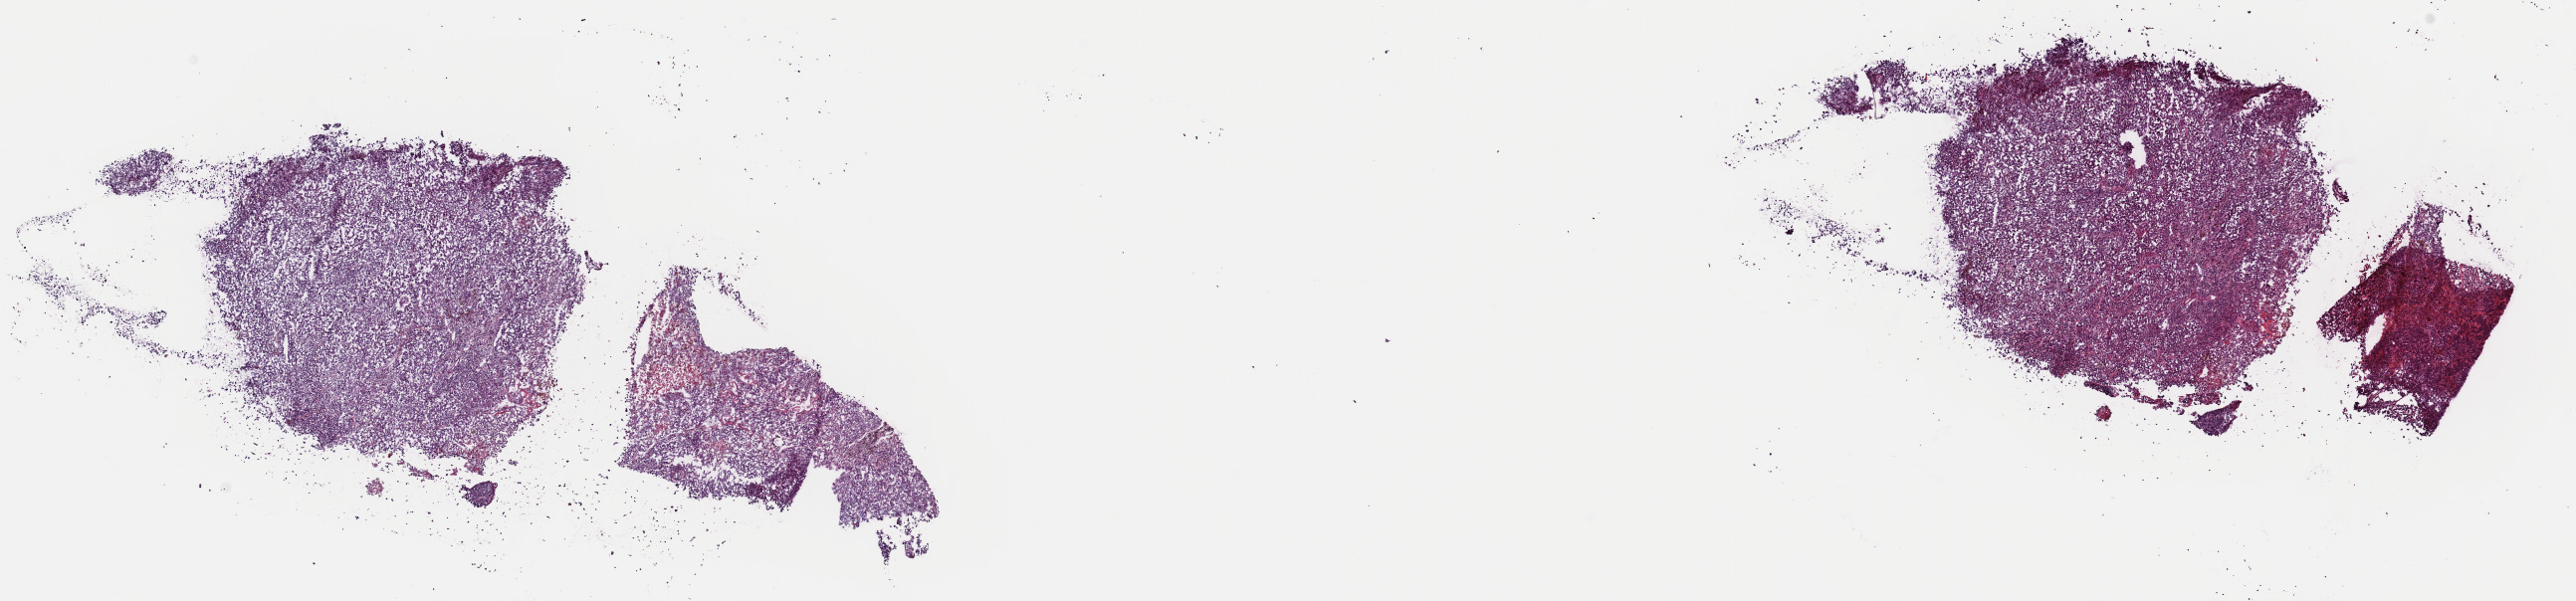
Whole-slide histology image, Hematoxylin and eosin (H&E) stained — whole scanned area (about 20.4 x 4.8 mm) shown as a low-resolution overview. Frozen section from the top of the tissue portion. Metastatic tumour sample, sampled site not recorded. Male patient; age at initial diagnosis 49 years. Pathologist review of this section (percent, as recorded): tumour cells 85%, tumour nuclei 80%, normal cells 0%, stromal cells 0%, necrosis 15%. Inflammatory infiltration, as recorded: lymphocyte infiltration 0%, monocyte infiltration 0%, neutrophil infiltration 0%.
- this section: metastatic tumour tissue
- patient diagnosis: Malignant melanoma, NOS